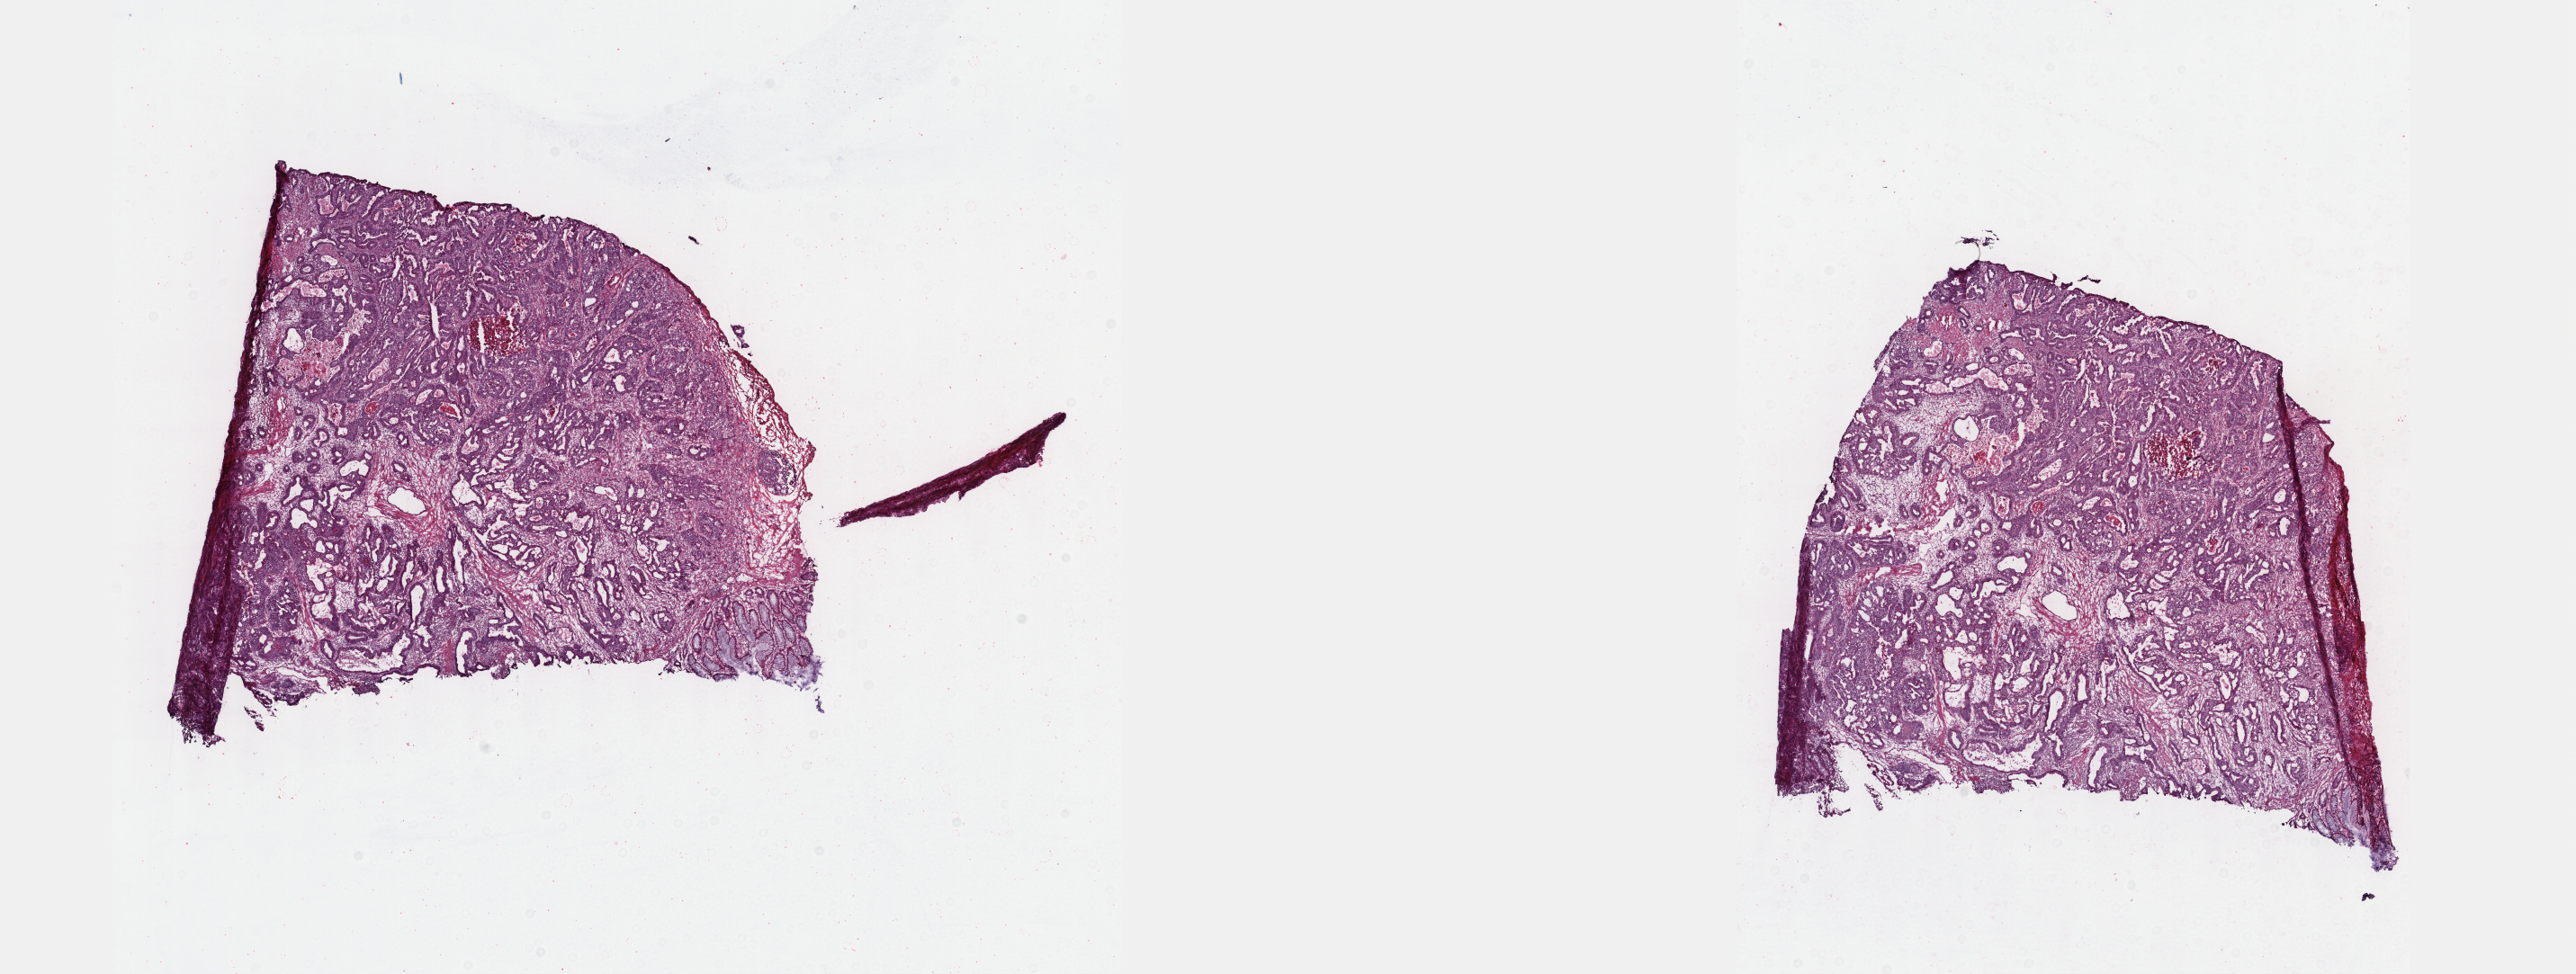
H&E whole-slide image — low-resolution overview of the scanned area, about 23.1 x 8.8 mm (acquisition: 40x scan), frozen section from the bottom of the tissue portion, sample: primary tumour, colon. Patient: female, age at initial diagnosis 74 years. Pathologist review of this section (percent, as recorded): tumour cells 75%, tumour nuclei 75%.
Diagnosis: Adenocarcinoma, NOS (sigmoid colon).